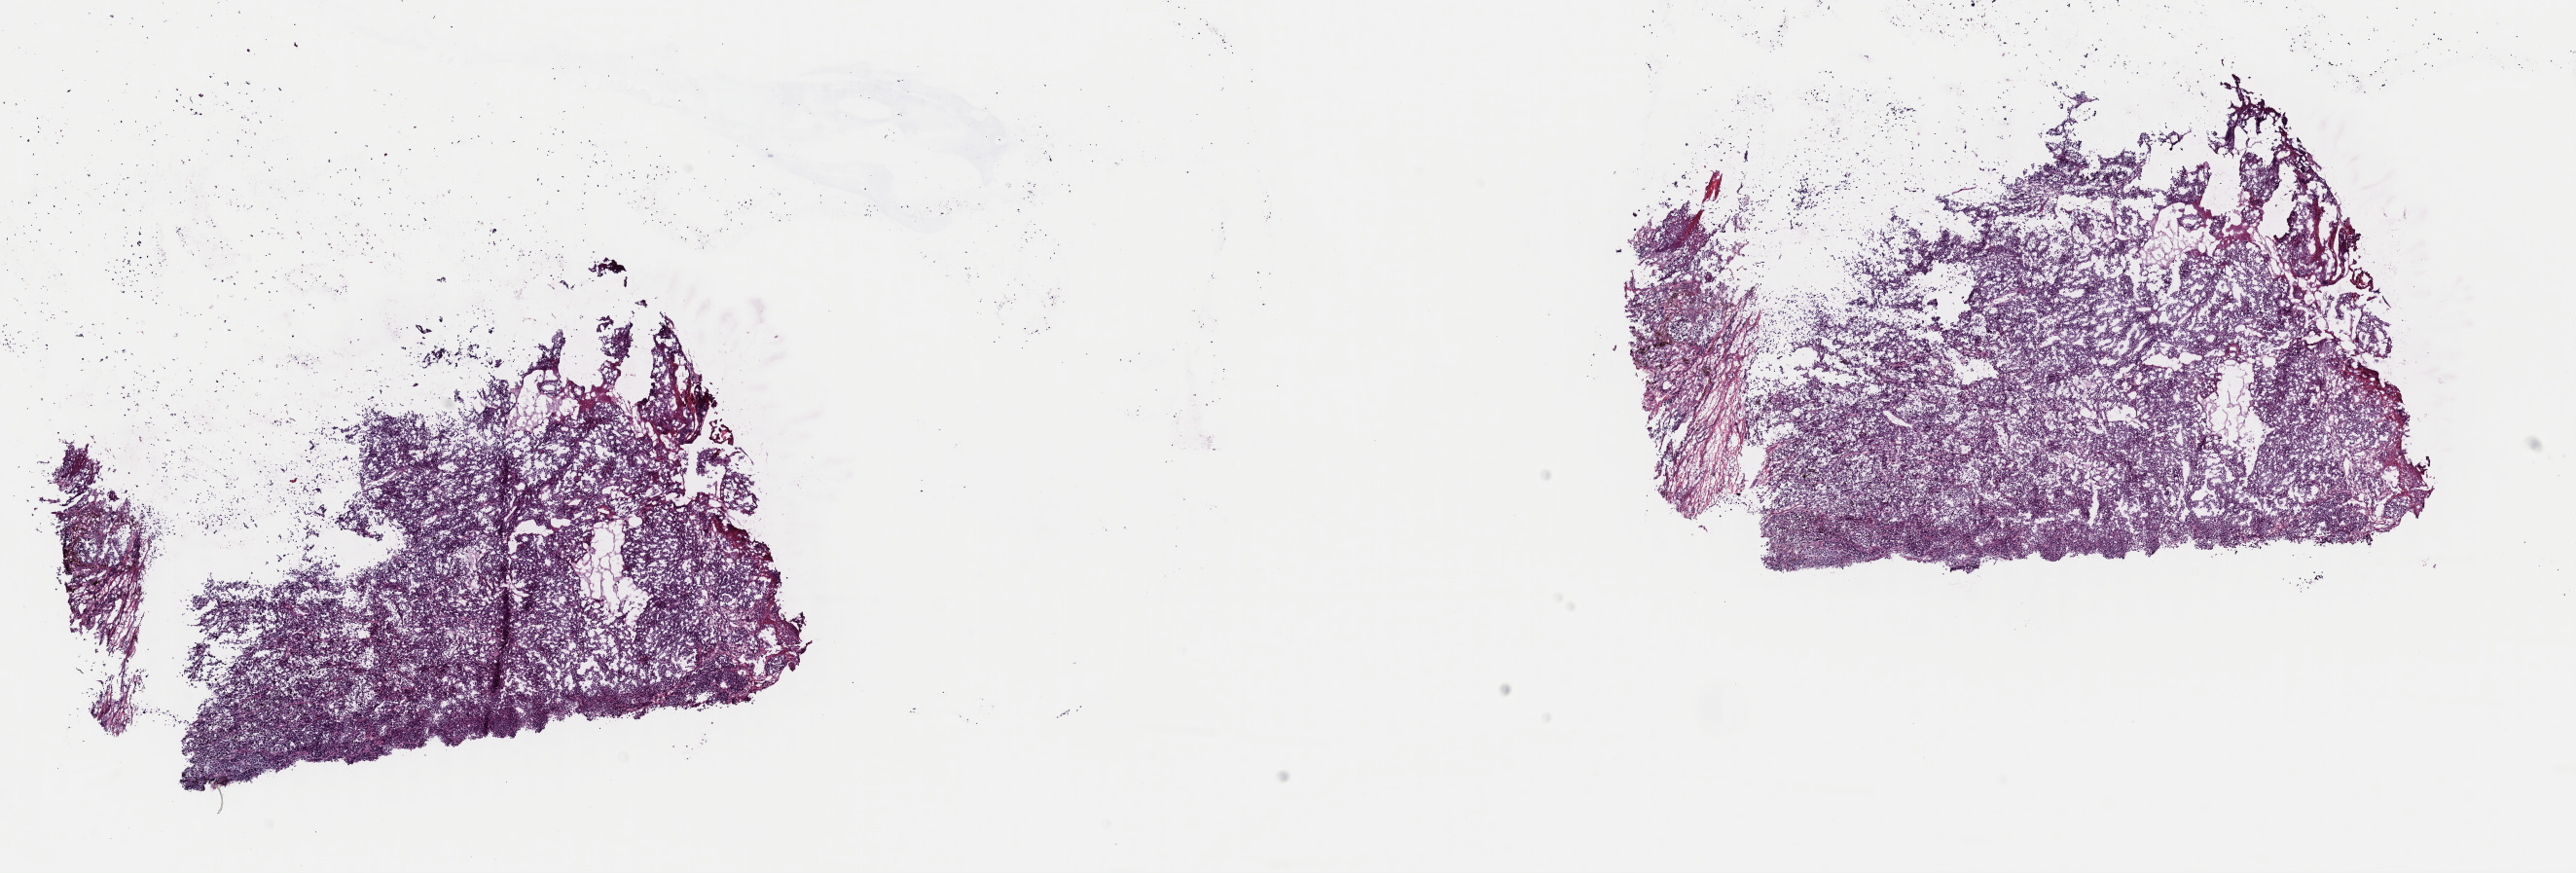
Whole-slide histology image, H&E, low-resolution overview of the scanned area, about 20.9 x 7.1 mm (acquisition: 40x scan), frozen section from the top of the tissue portion, sample: primary tumour, skin. Patient: male, age at initial diagnosis 57 years. Pathologist review of this section (percent, as recorded): tumour cells 100%, tumour nuclei 95%, normal cells 0%, stromal cells 0%, necrosis 0%. Infiltration values recorded for this section: lymphocyte infiltration 0%, monocyte infiltration 0%, neutrophil infiltration 0%.
Histologic diagnosis: Malignant melanoma, NOS. AJCC pathologic stage: IIC (7th edition).